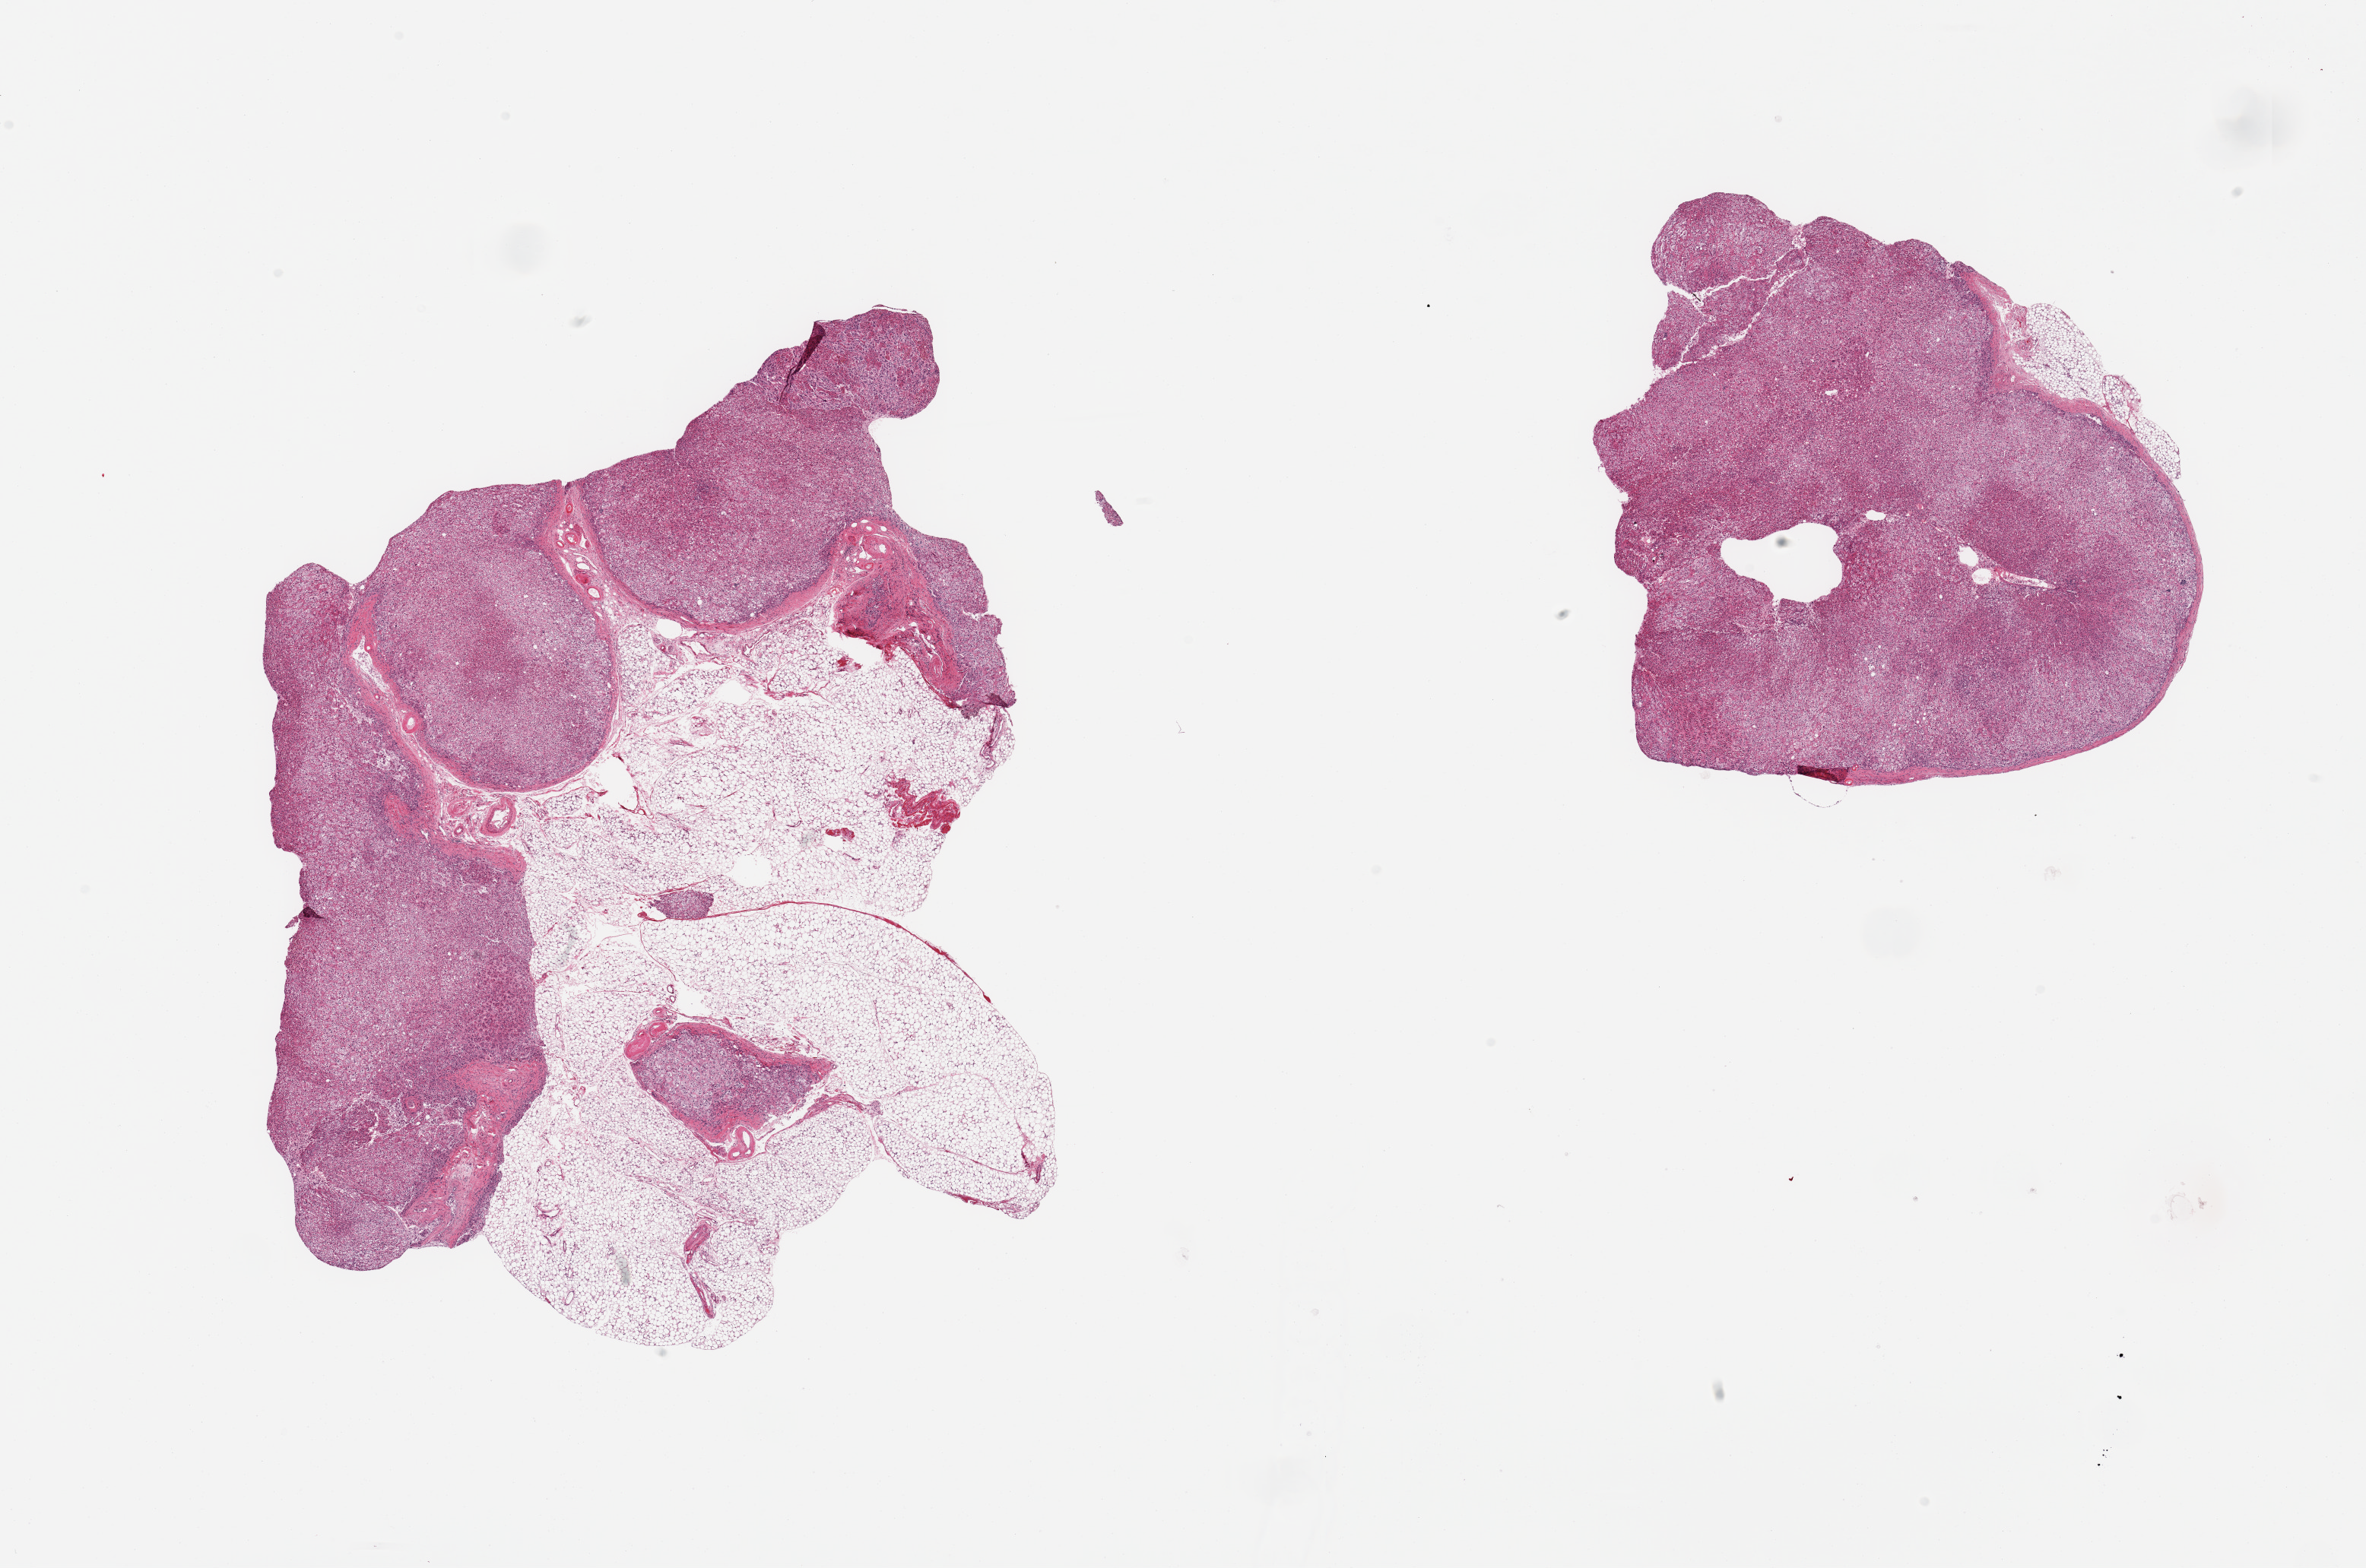
Haematoxylin and eosin whole-slide image, low-resolution overview of the scanned area, about 24.6 x 16.3 mm; PAXgene-fixed, paraffin-embedded tissue; sampled site (target tissue): adrenal gland; tissue donor sample. Donor sex: female.
Review note (as recorded): 2 pieces; 1 with 50% external adipose tissue, other with 5%.